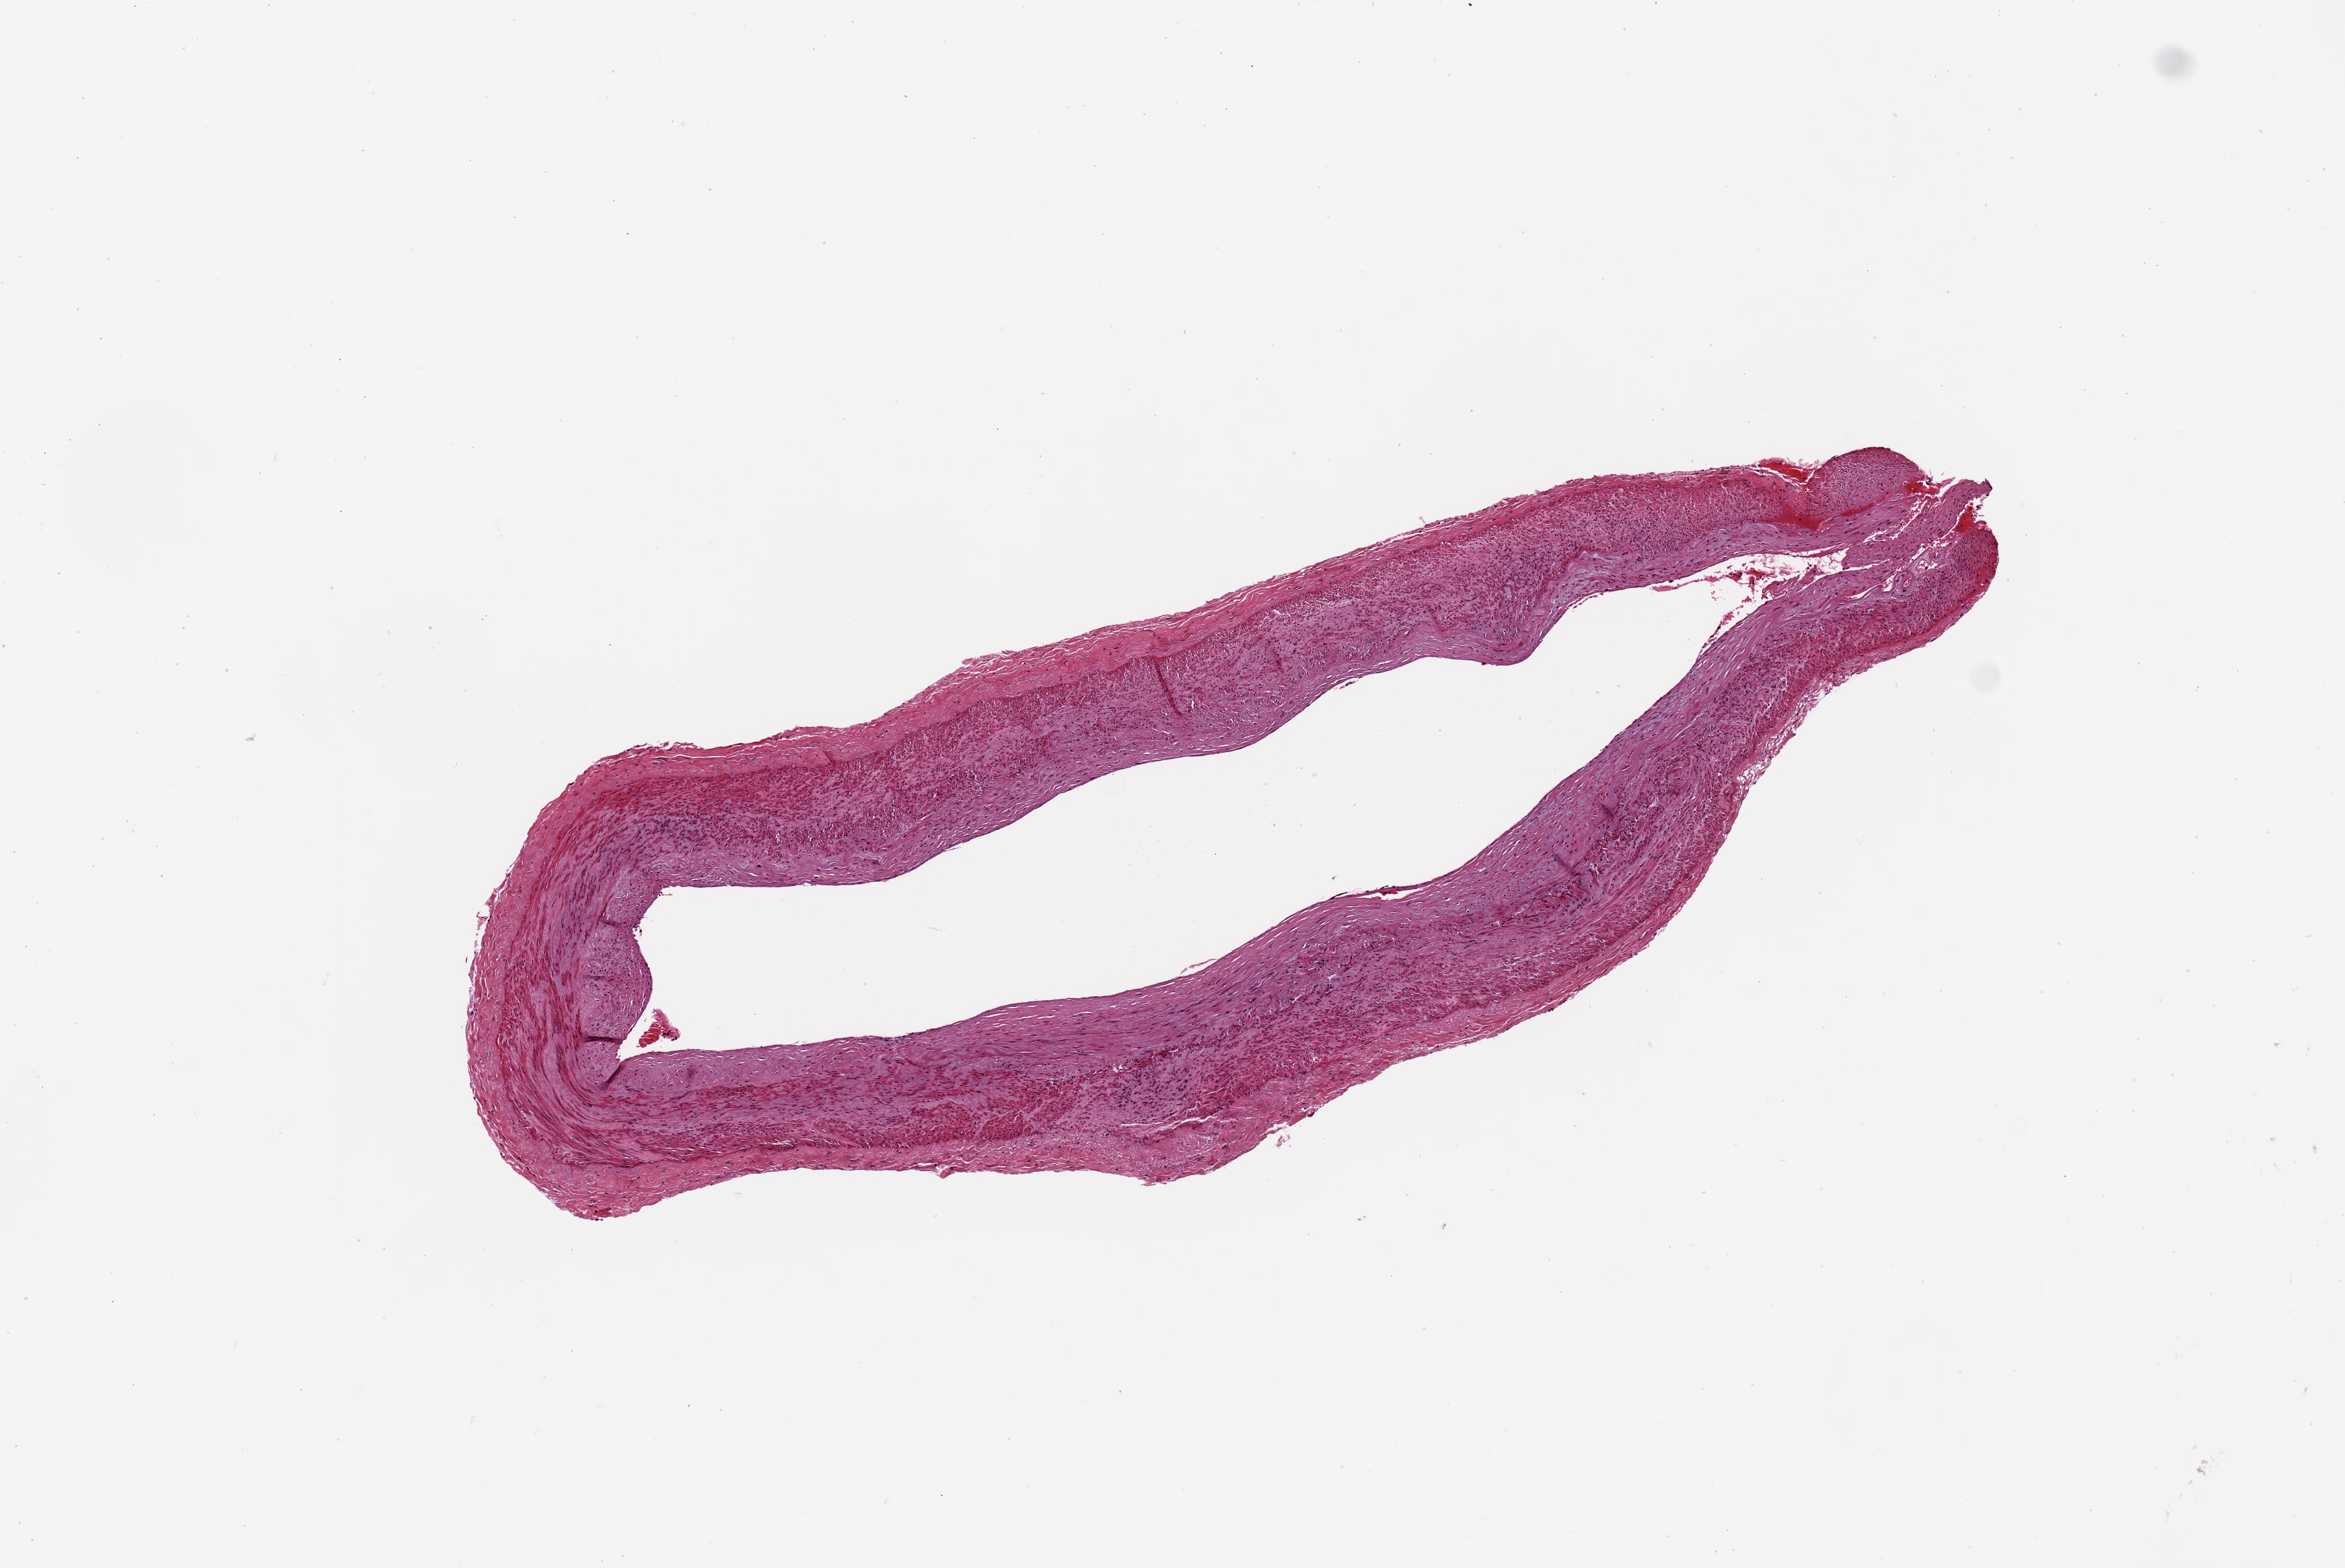
Whole-slide image, H&E stain, brightfield, a low-resolution overview of the entire scanned area, about 6.9 x 4.6 mm; PAXgene-fixed, paraffin-embedded tissue; section of tibial artery (target tissue); donor tissue sample. Female donor.
- review note (as recorded): 4.7x1.5mm. Good clean specimen, minimal atherosclerotic damage